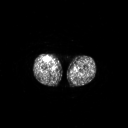
FDG PET of an extremity soft-tissue mass (from a PET/CT study), one axial slice. 128 × 128 image matrix, field of view 700 × 700 mm. Patient: male, 56 years. From the clinical record (not read from this slice): histological type: pleiomorphic leiomyosarcoma; grade: intermediate; site of the primary tumour: right thigh.
Outlined on this slice (expert contour drawn on MRI and transferred to this co-registered scan by the dataset authors):
- gross tumour volume including surrounding oedema: bounding box (x1, y1, x2, y2) in pixels: (43, 56, 51, 62)